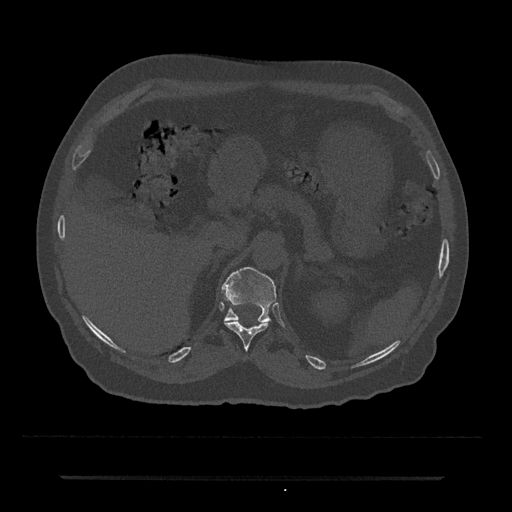
CT including the spine, one axial slice. Position 158 of 797 along the scan axis. Reconstruction kernel Br40s/3. Bone window (W 1800 / L 400 HU). 0.5 mm slice thickness. 512 × 512 image matrix, field of view 437 × 437 mm. Patient: male, 69 years. Case-level facts recorded for this patient, not image findings: primary cancer: prostate.
Annotated regions visible in this slice (semi-automatic segmentation, software-assisted and operator-edited):
- T11 vertebra: box from (x=225, y=321) to (x=268, y=350) px
- T12 vertebra: (x=222, y=267)–(x=276, y=322)